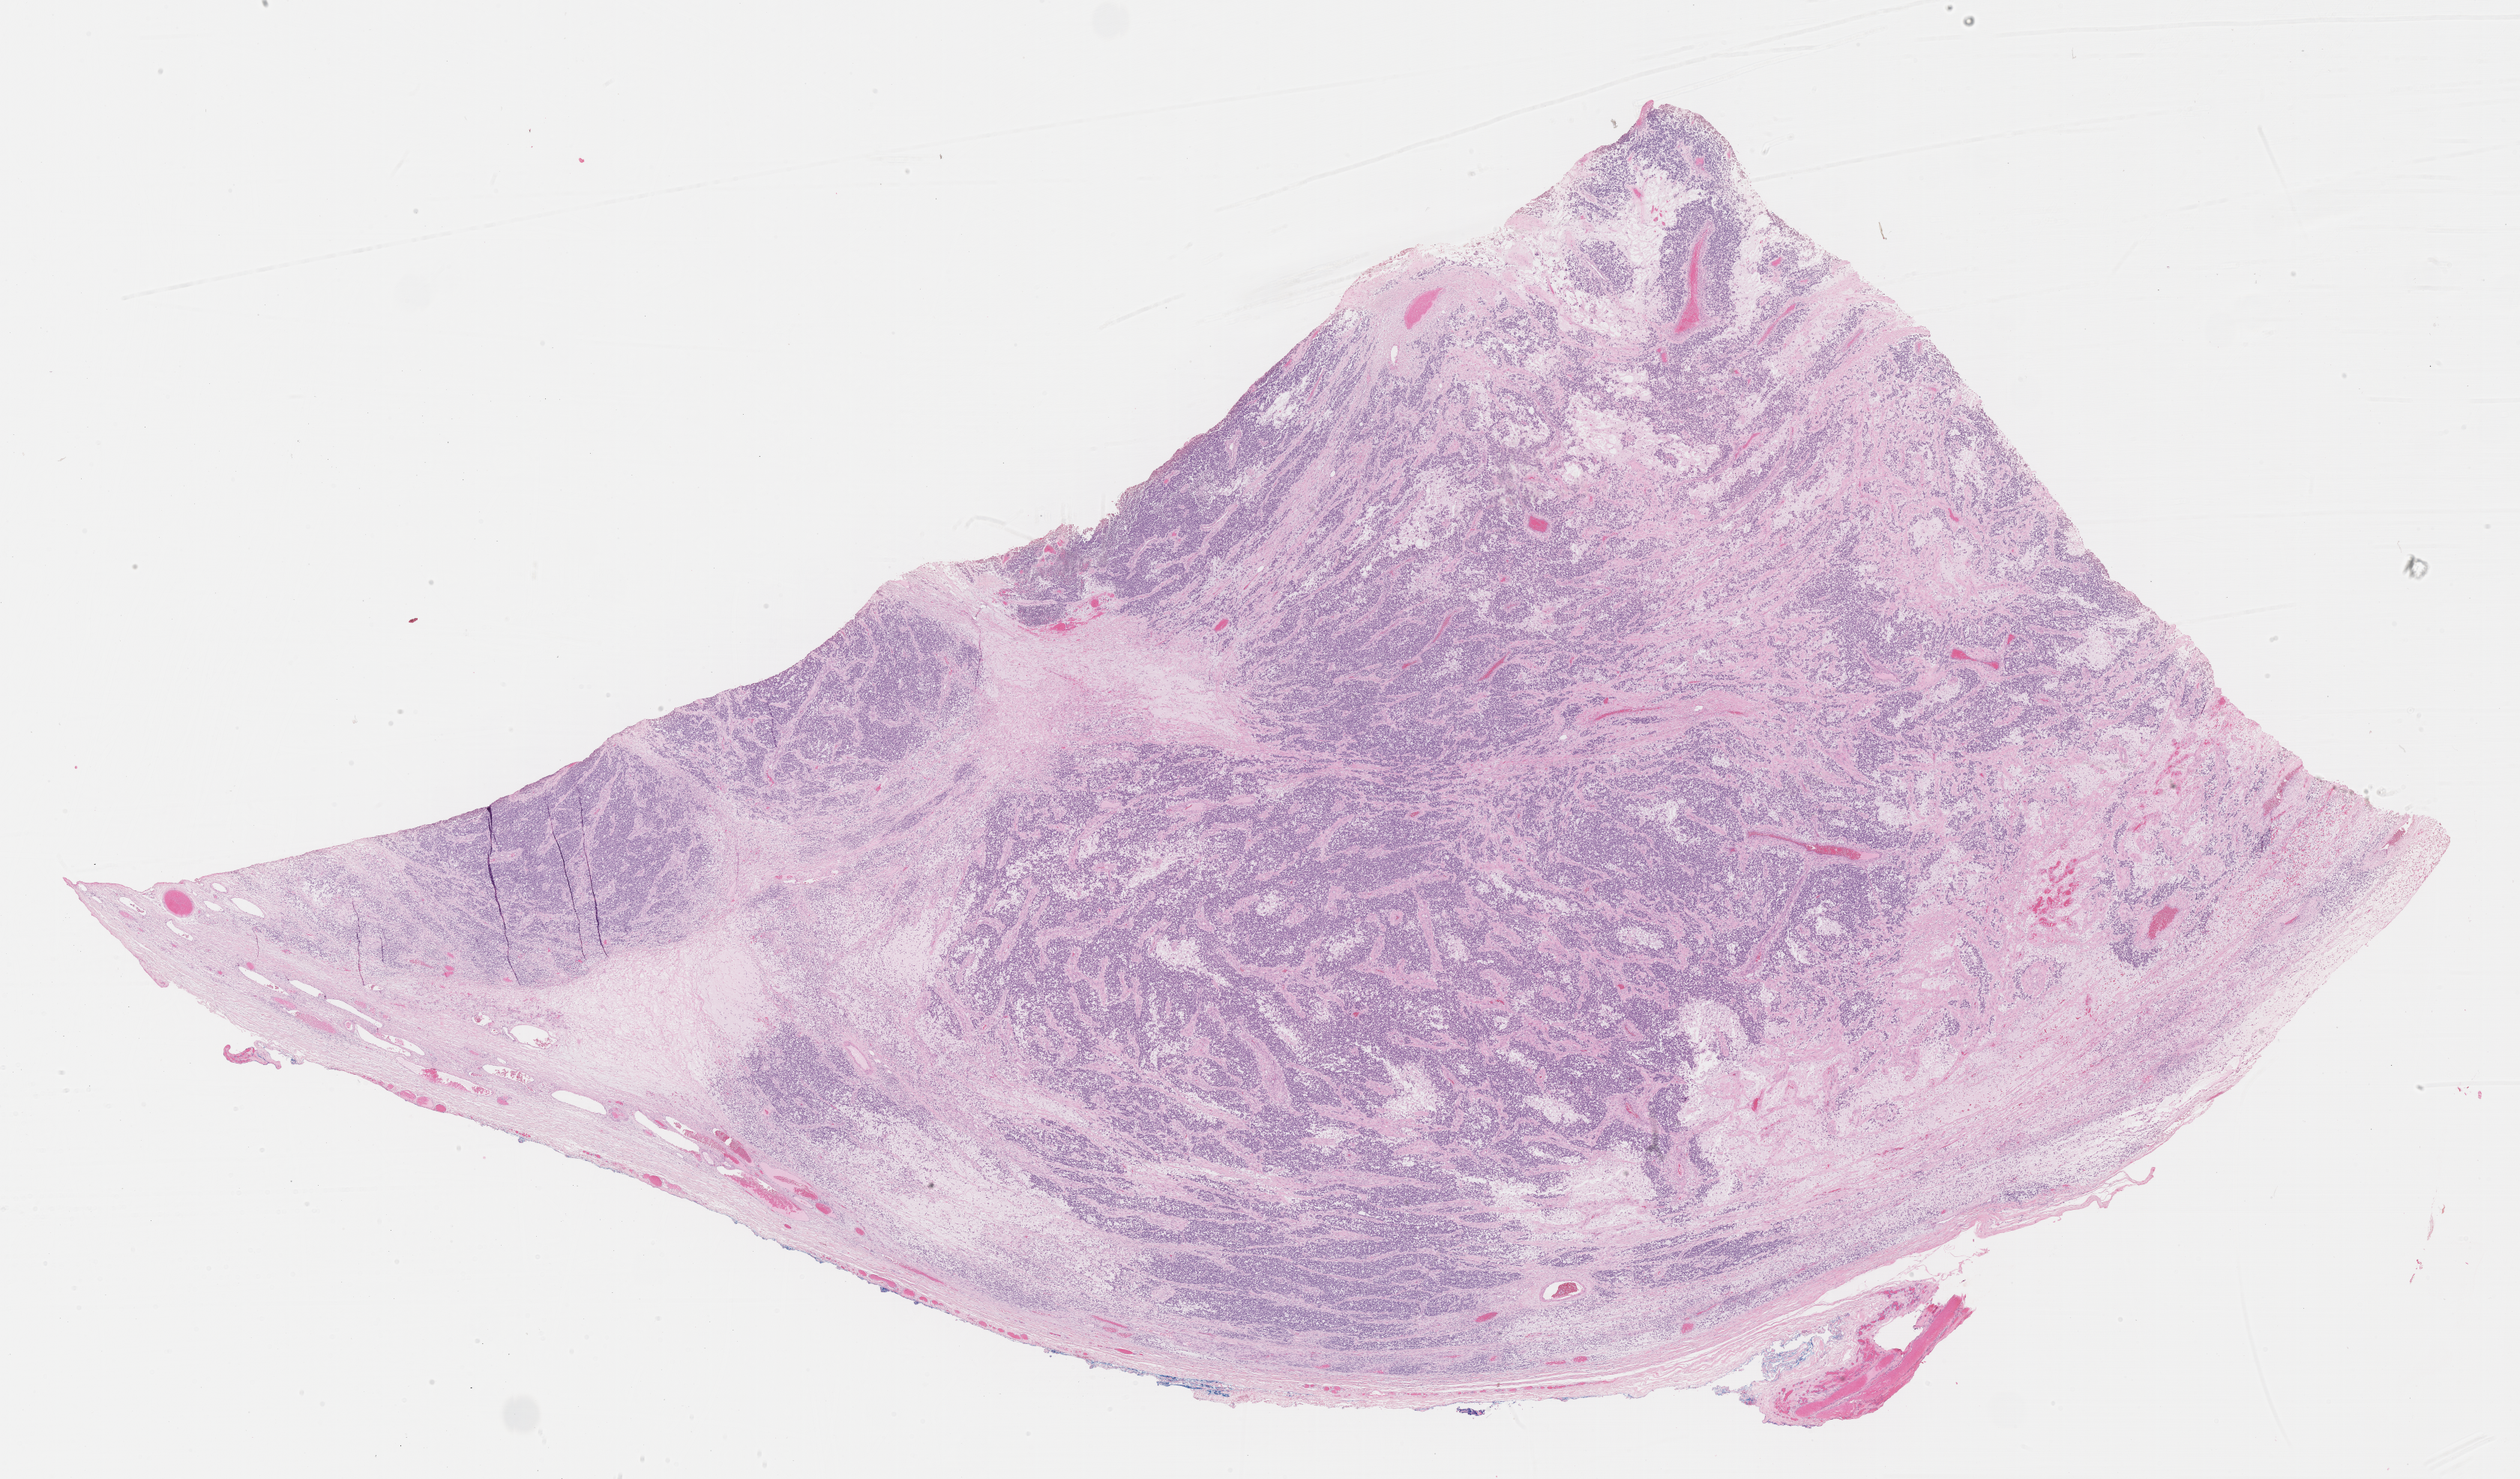
Whole-slide image, H&E stain of tumor tissue, a low-resolution overview of the entire scanned area, about 27.2 x 15.9 mm, formalin-fixed paraffin-embedded section, sample anatomic site: testicle, right. Male patient, age at diagnosis 16.2 years.
* diagnosis: rhabdomyosarcoma; histological classification: embryonal rhabdomyosarcoma
* metastatic status at presentation (as recorded): non-metastatic (unconfirmed)